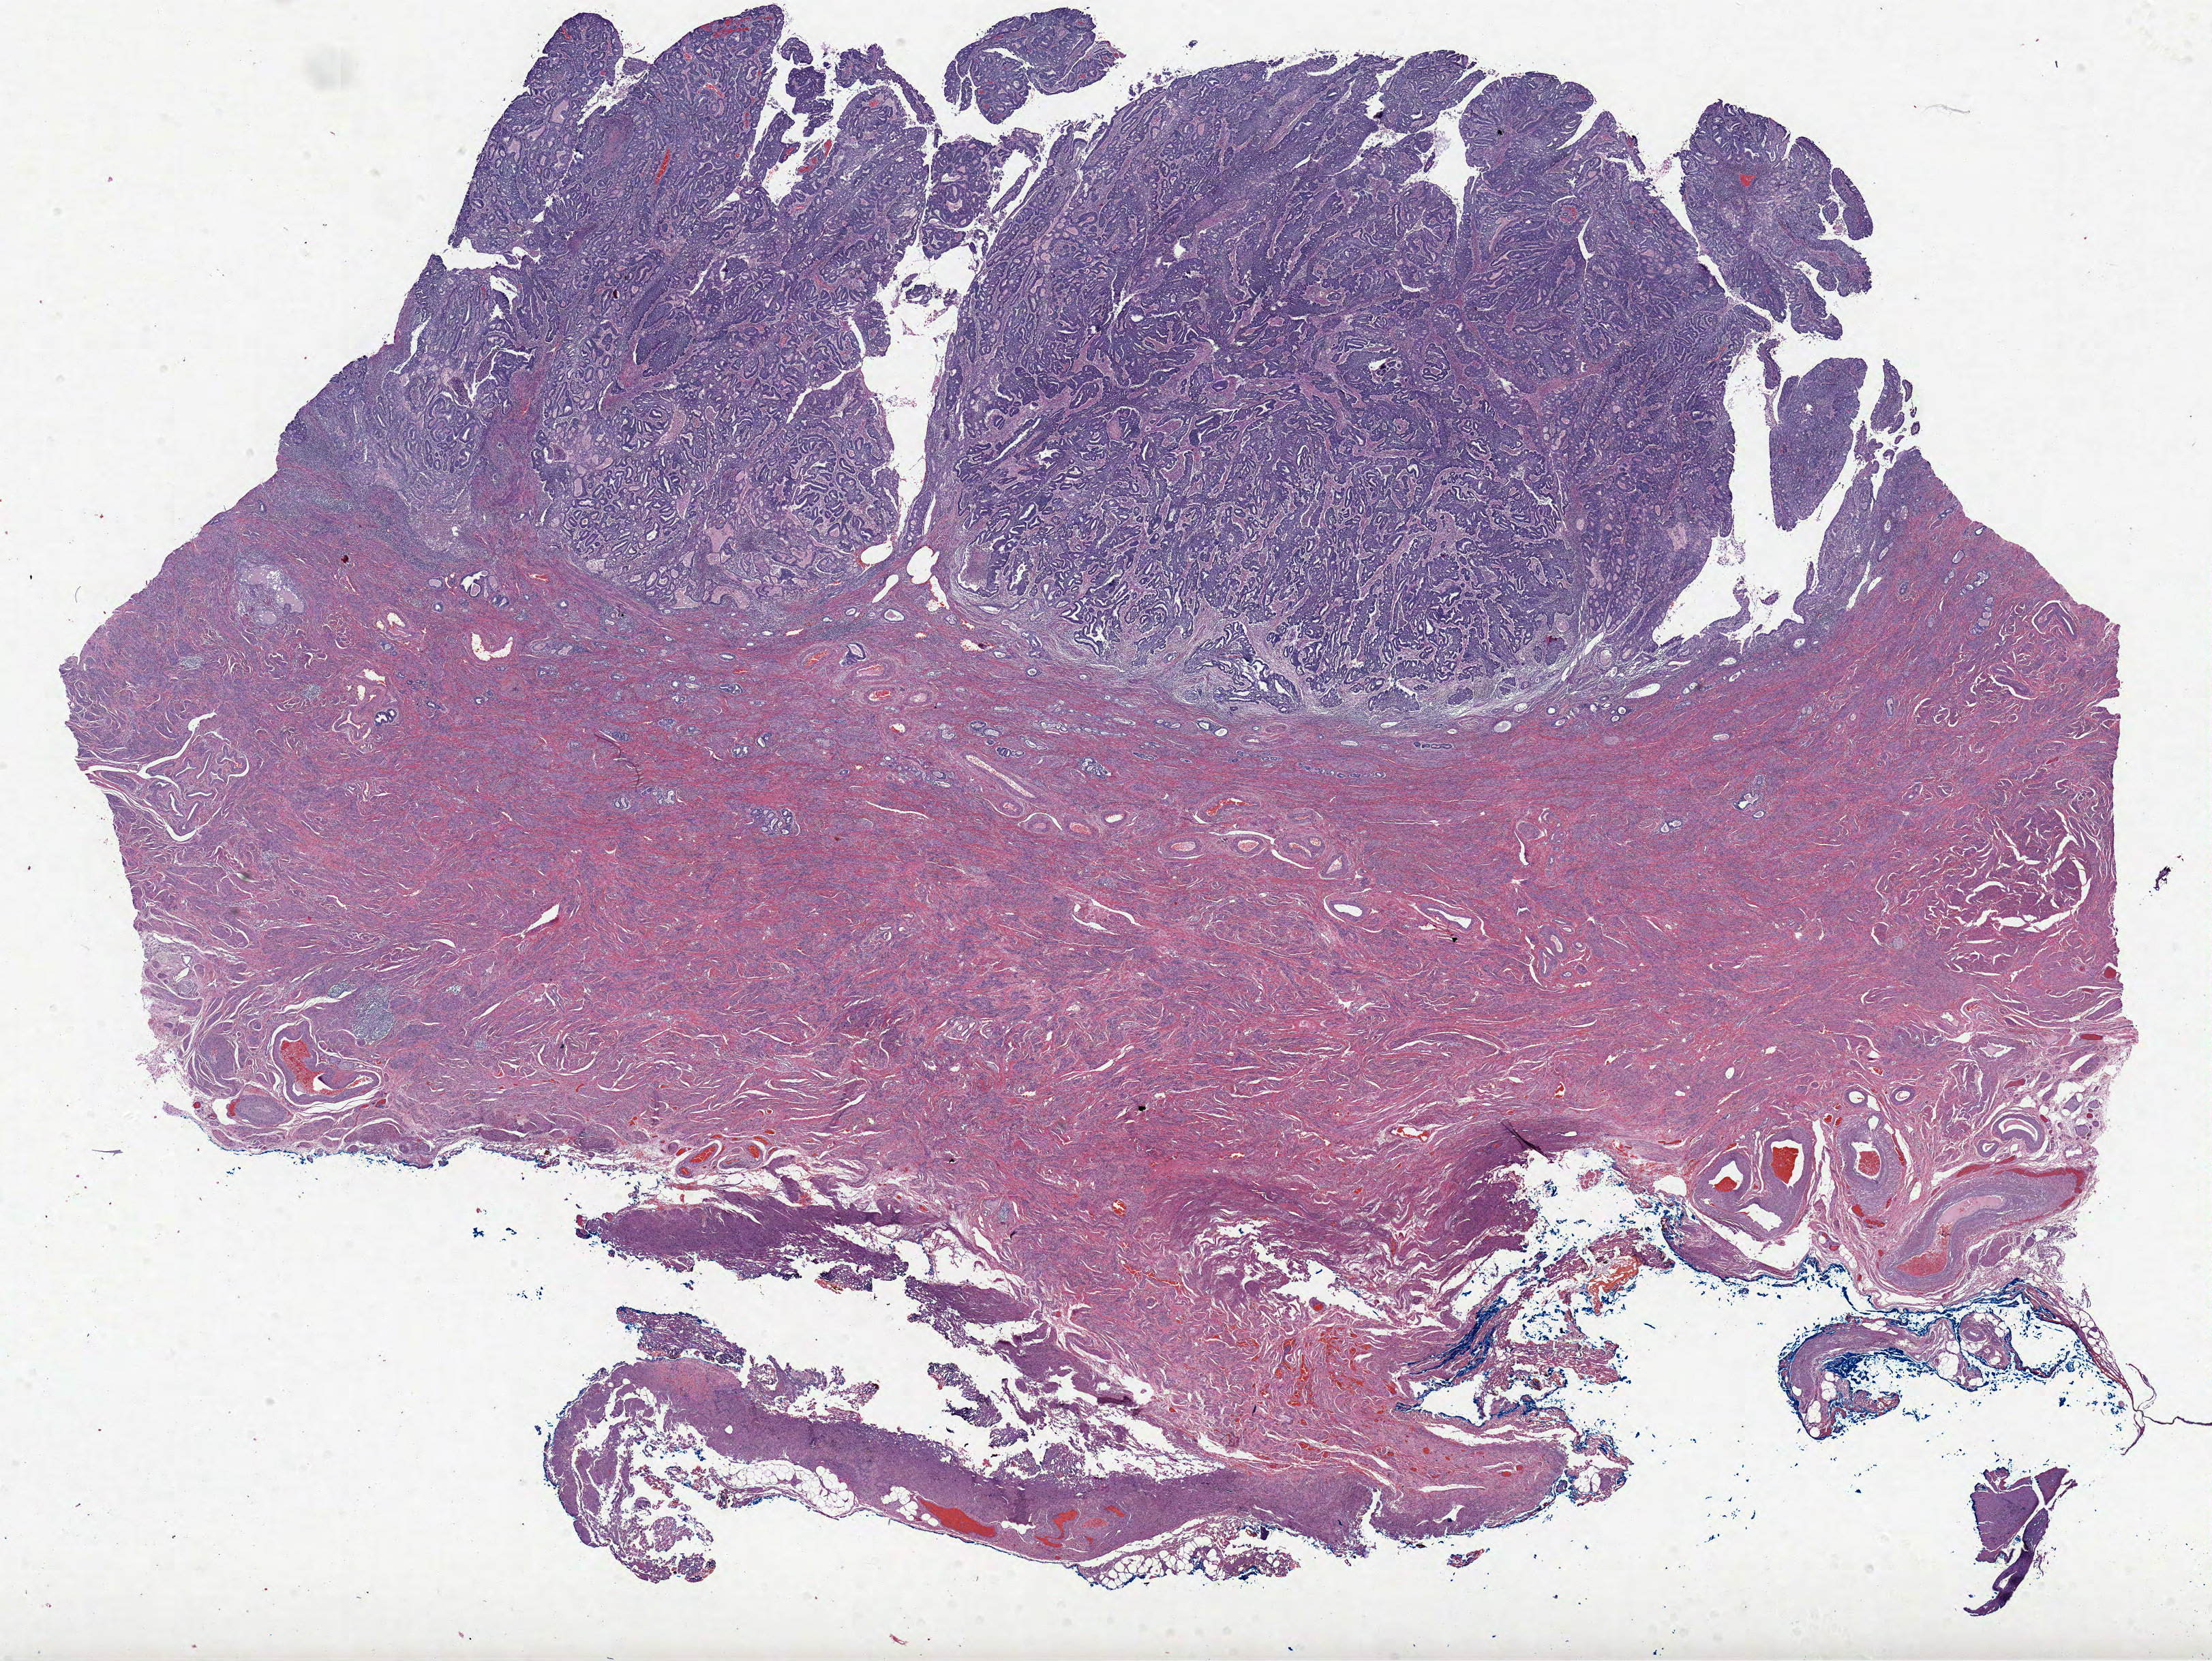
Hematoxylin and eosin (H&E) stained whole-slide image, shown as a low-resolution overview of the whole scanned area (about 25.9 x 19.4 mm, slide scanned at 20x); FFPE section; primary tumour sample from the uterus. Patient: female, age at initial diagnosis 57 years. Histologic grade: G2 (moderately differentiated).
FIGO stage: II. Lymph nodes positive (case pathology): 0 of 16 examined. Pathologic diagnosis: Endometrioid adenocarcinoma, NOS.